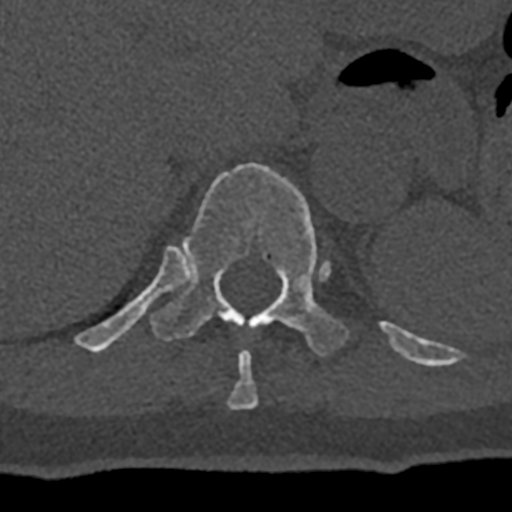
CT including the spine, one axial slice; slice 556 of 797 in the series (ordered by position); reconstruction kernel Br40s/3; bone window (W 1800 / L 400 HU); 0.5 mm slice thickness; 512 × 512 image matrix, field of view 160 × 160 mm. Male patient, age 74 years. Case-level facts recorded for this patient, not image findings: primary cancer: renal.
Outlined on this slice (semi-automatic segmentation, software-assisted and operator-edited):
- T10 vertebra: box from (x=227, y=350) to (x=259, y=409) px
- T11 vertebra: (x=74, y=163)–(x=432, y=367)